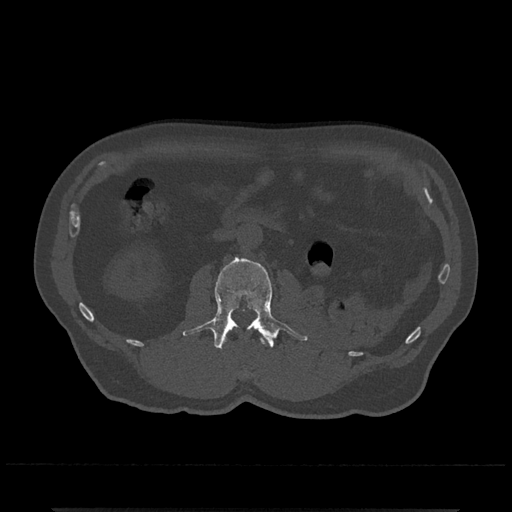
CT including the spine, one axial slice. Position 300 of 797 along the scan axis. Bone window (W 1800 / L 400 HU). 0.5 mm slice thickness. 512 × 512 image matrix, field of view 393 × 393 mm. Male patient, age 67 years. From the clinical record (not read from this slice): primary cancer: prostate.
Structures marked on this image (semi-automatically segmented with operator editing):
- L1 vertebra: box from (x=260, y=338) to (x=266, y=345) px
- L2 vertebra: (x=182, y=258)–(x=308, y=349)